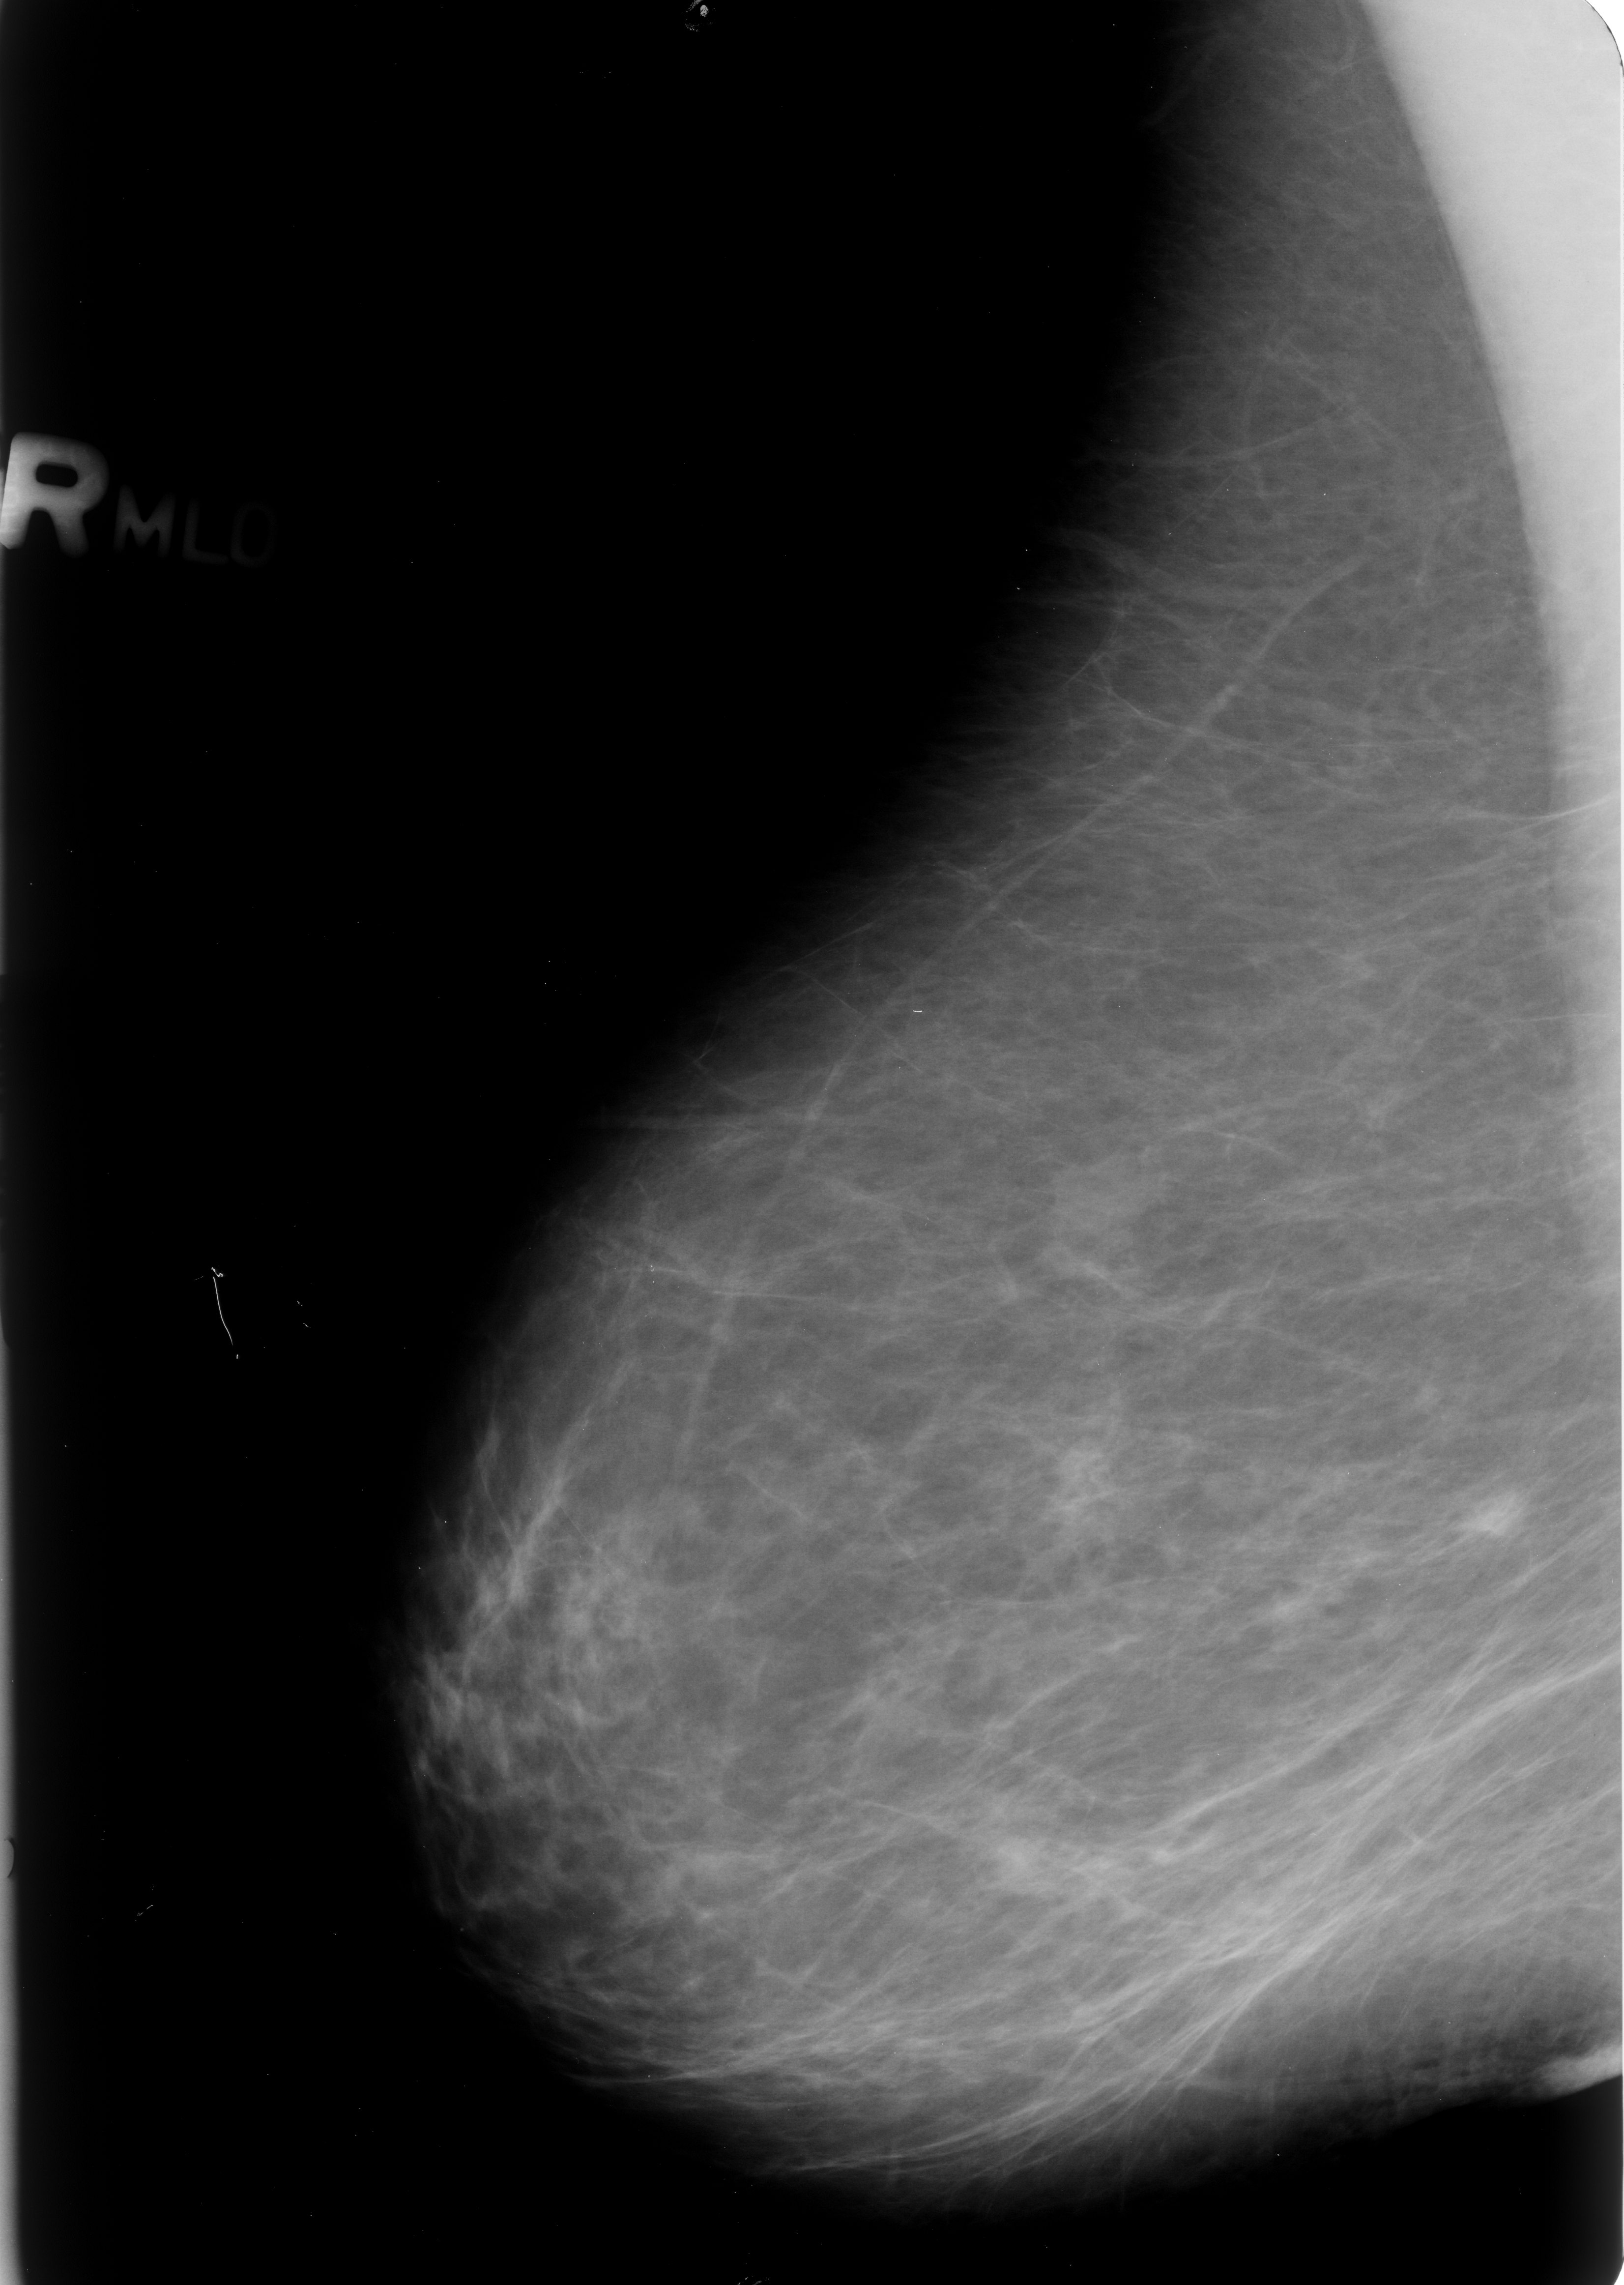
Digitized screen-film mammogram. Right breast. Mediolateral oblique (MLO) view. 1624 × 2285 image matrix.
Expert-marked regions of interest on this image (one box per marked abnormality):
- mass, shape oval, margins ill defined; BI-RADS assessment category 4; subtlety rating 4 on a 1 (subtle) to 5 (obvious) scale; pathology (as recorded): malignant: bounding box <1443,1467,1541,1556> (left, top, right, bottom; pixels)